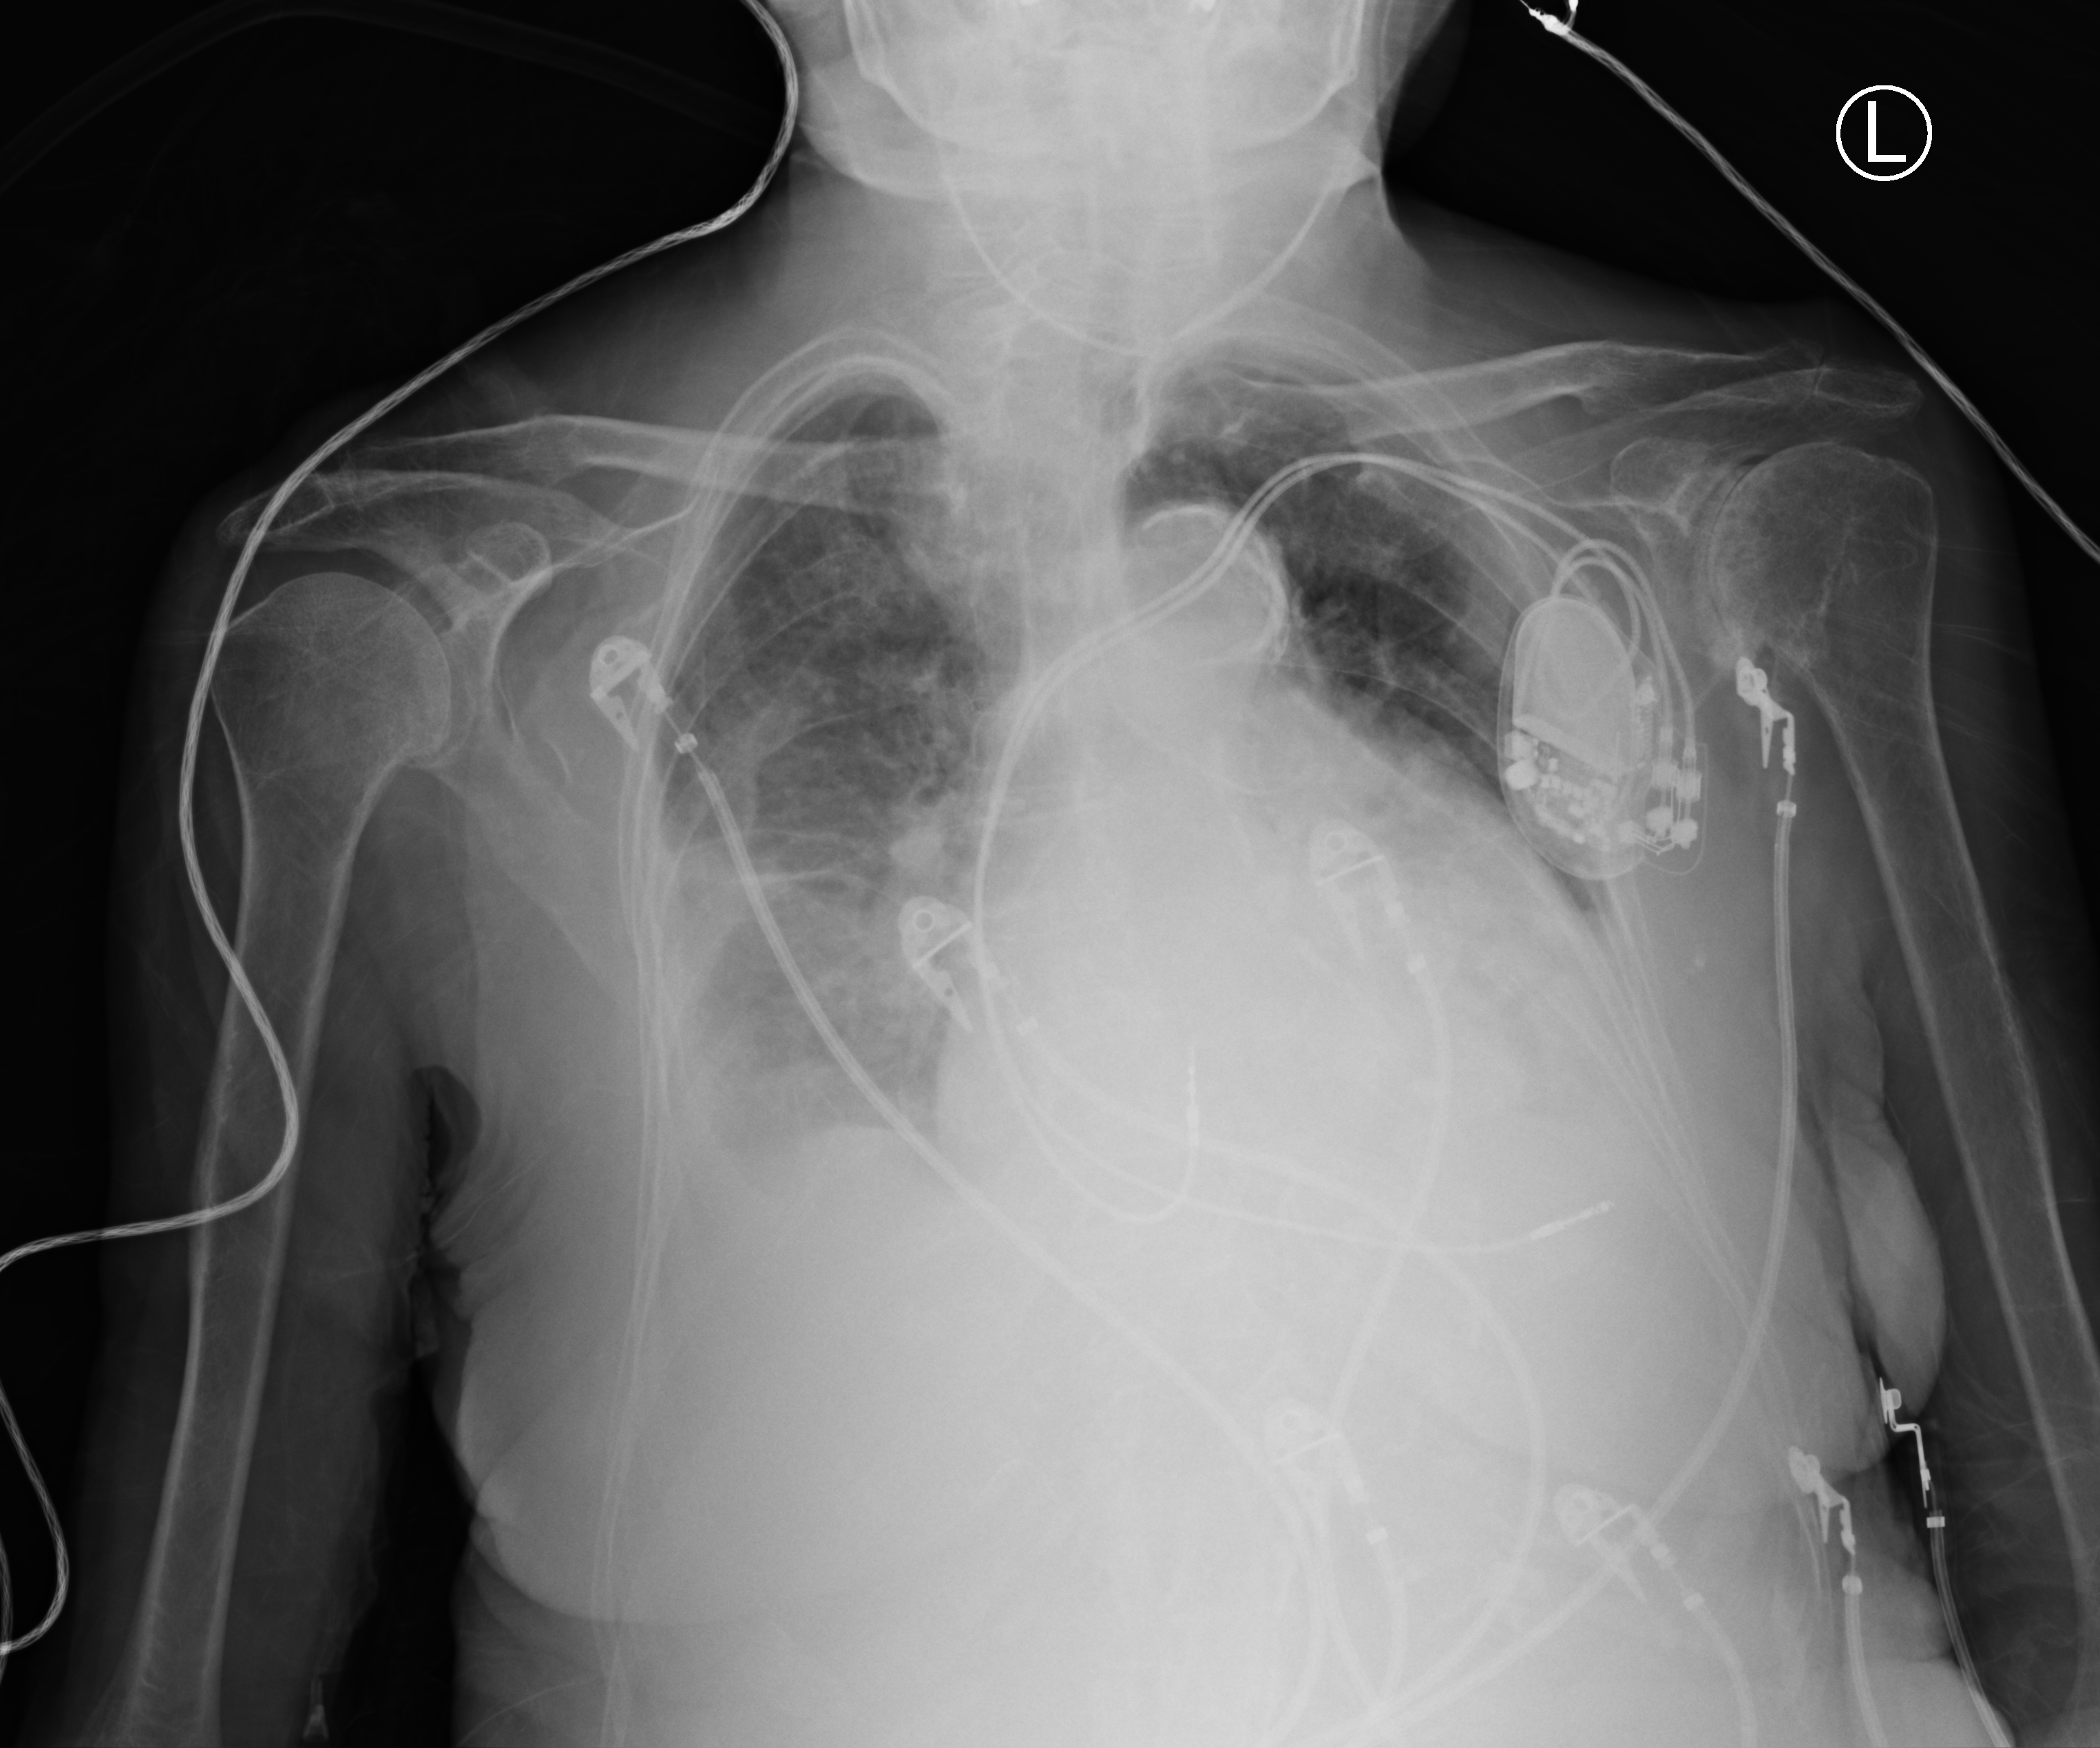
Chest X-ray (portable); anteroposterior (AP) projection. Female patient hospitalised with COVID-19, age 75–90 years.
From the hospital-stay record, not from the radiograph (when in the stay this image was taken is not recorded):
- length of hospital stay: 5 days
- hypertension (admission record): yes